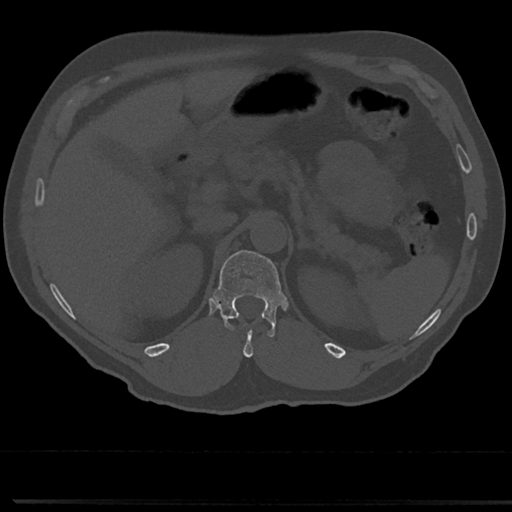
CT including the spine, one axial slice. Slice 162 of 817 in the series (ordered by position). Reconstruction kernel Br40s/3. 120 kVp. Bone window (W 1800 / L 400 HU). 512 × 512 image matrix, field of view 355 × 355 mm. Patient: male, 61 years. From the clinical record (not read from this slice): primary cancer: prostate.
Annotated regions visible in this slice (semi-automatic segmentation, software-assisted and operator-edited):
- T11 vertebra: bounding box [x1, y1, x2, y2] px = [246, 349, 250, 355]
- T12 vertebra: [217, 249, 283, 335]